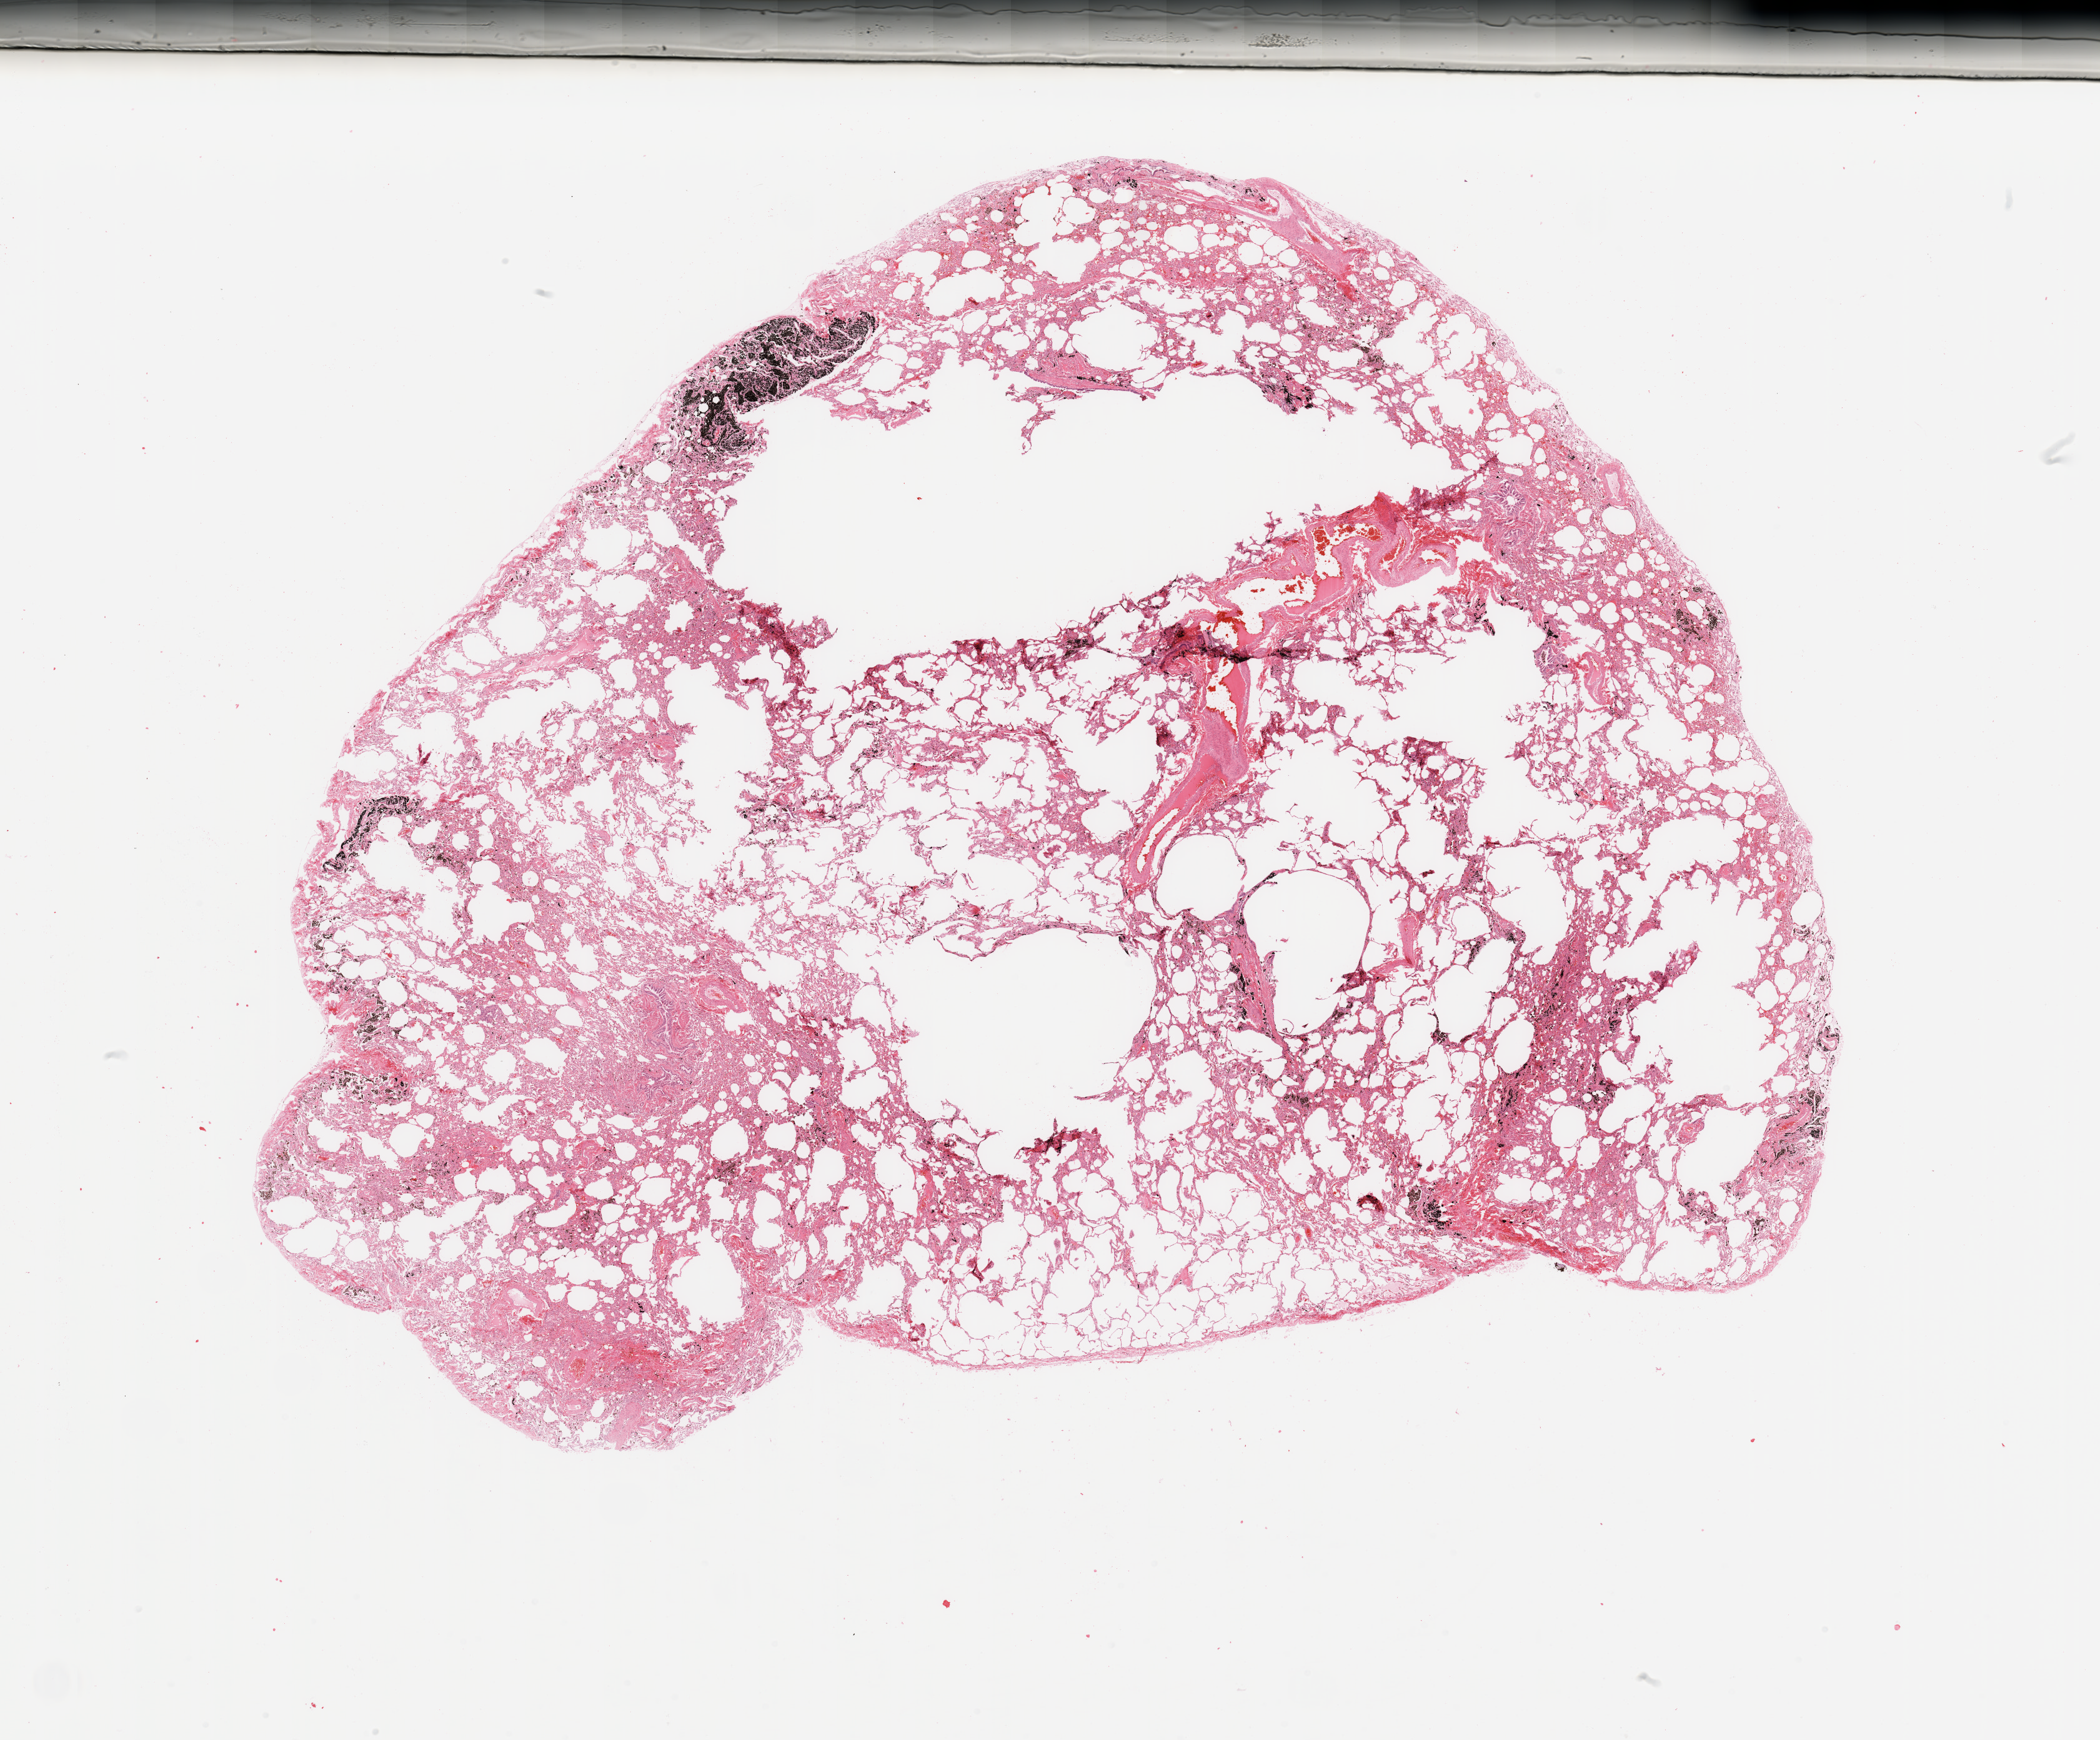
Whole-slide histology image, H&E, shown as a low-resolution overview of the whole scanned area (about 26.6 x 22.0 mm), normal (non-tumour) tissue sample, sampled site: lung. Male, 52 y/o.
This section: normal (non-tumour) tissue from the same patient. Patient diagnosis: Squamous cell carcinoma, NOS.